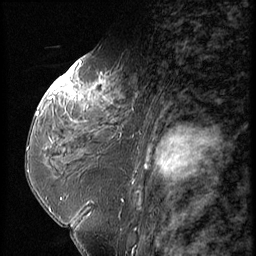
Breast MRI (dynamic contrast-enhanced), one sagittal slice. Slice 32 of 56 in the series (ordered by position). Dynamic contrast-enhanced series, image 2 of 3 at this slice position (ordered by acquisition). 1.5 T. TE 4.2 ms, TR 9 ms. 256 × 256 image matrix, field of view 180 × 180 mm. Patient: female, 59 years. From the clinical record (not read from this slice): setting: breast cancer imaged before/during neoadjuvant chemotherapy; receptor status: HER2-positive.
Outlined on this slice (semi-automatic segmentation, software-assisted and operator-edited):
- analysis volume of interest (the breast-tissue region the enhancement analysis was run in; not a lesion): bounding box <44,66,151,135> (left, top, right, bottom; pixels)
- tumour enhancement mask (voxels above the 140 % enhancement threshold inside the analysis volume of interest): <50,66,107,98>